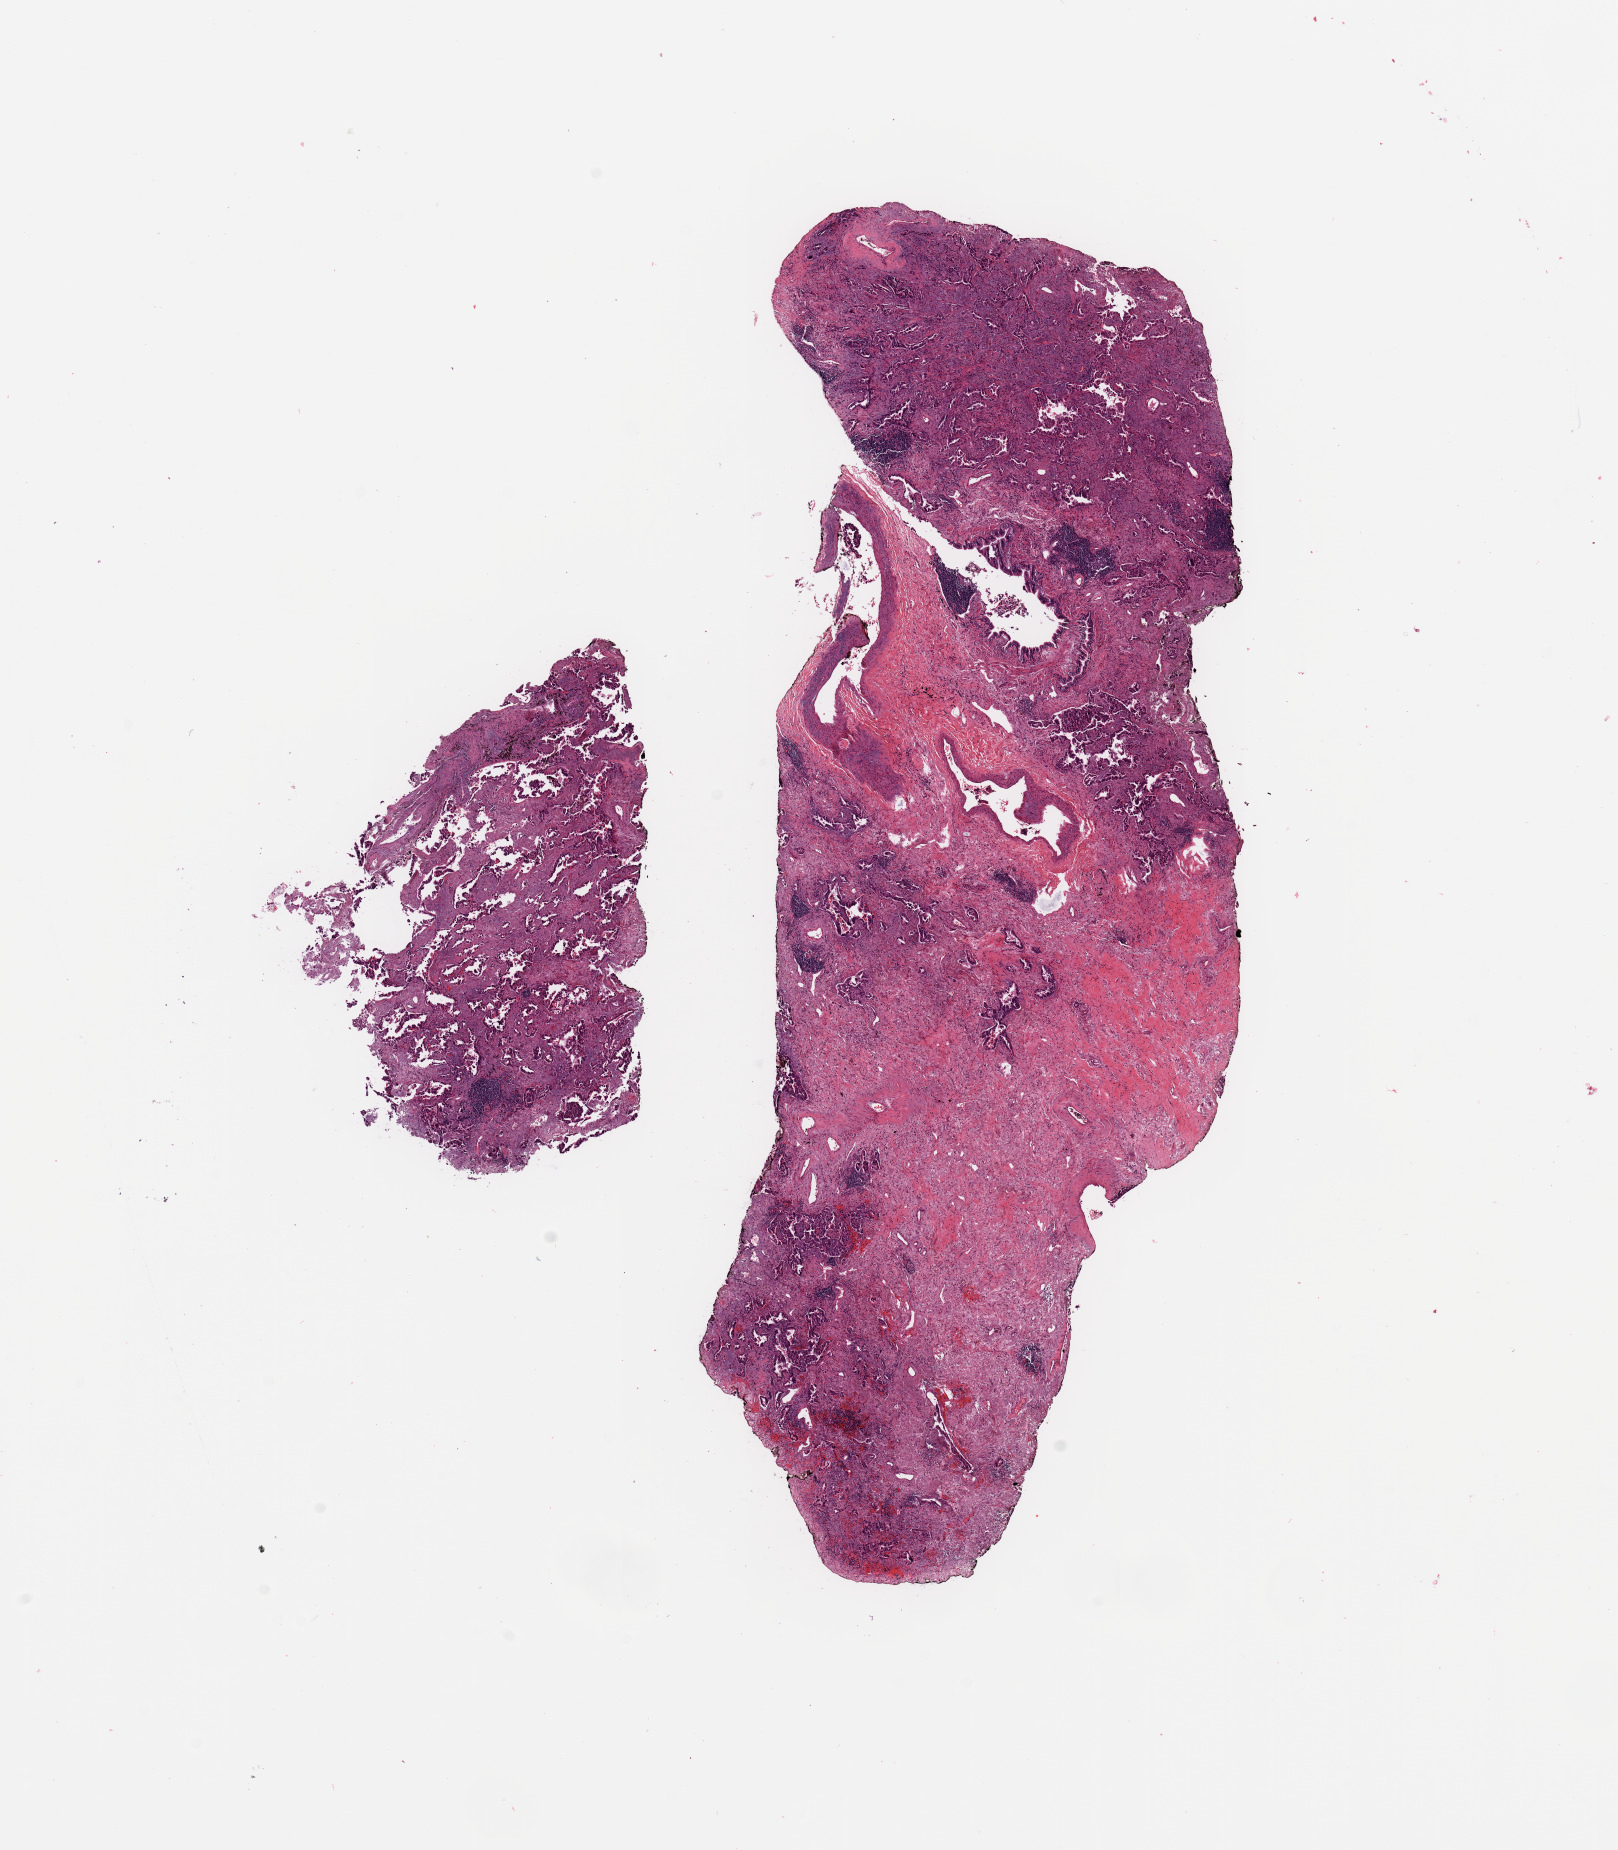
Whole-slide histology image, H&E, low-resolution overview of the scanned area, about 12.8 x 14.6 mm, lung, tumour tissue. Patient: female, age 67 years. Histologic grade: G2 (moderately differentiated).
Histologic diagnosis: Adenocarcinoma, NOS. AJCC pathologic stage: IB. Primary tumour site (as recorded): left upper lobe.